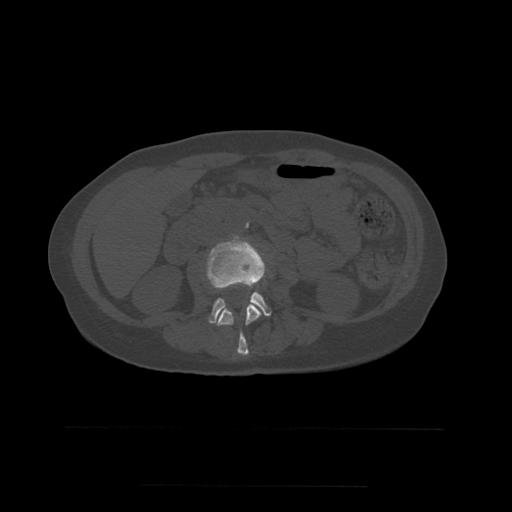
CT including the spine, one axial slice. Slice 199 of 544 in the series (ordered by position). Bone window (W 1800 / L 400 HU). 1.25 mm slice thickness. 512 × 512 image matrix, field of view 350 × 350 mm. Patient age 58 years. From the clinical record (not read from this slice): primary cancer: lung.
Structures marked on this image (semi-automatically segmented with operator editing):
- L2 vertebra: bounding box <217,236,262,356> (left, top, right, bottom; pixels)
- L3 vertebra: <207,237,272,324>